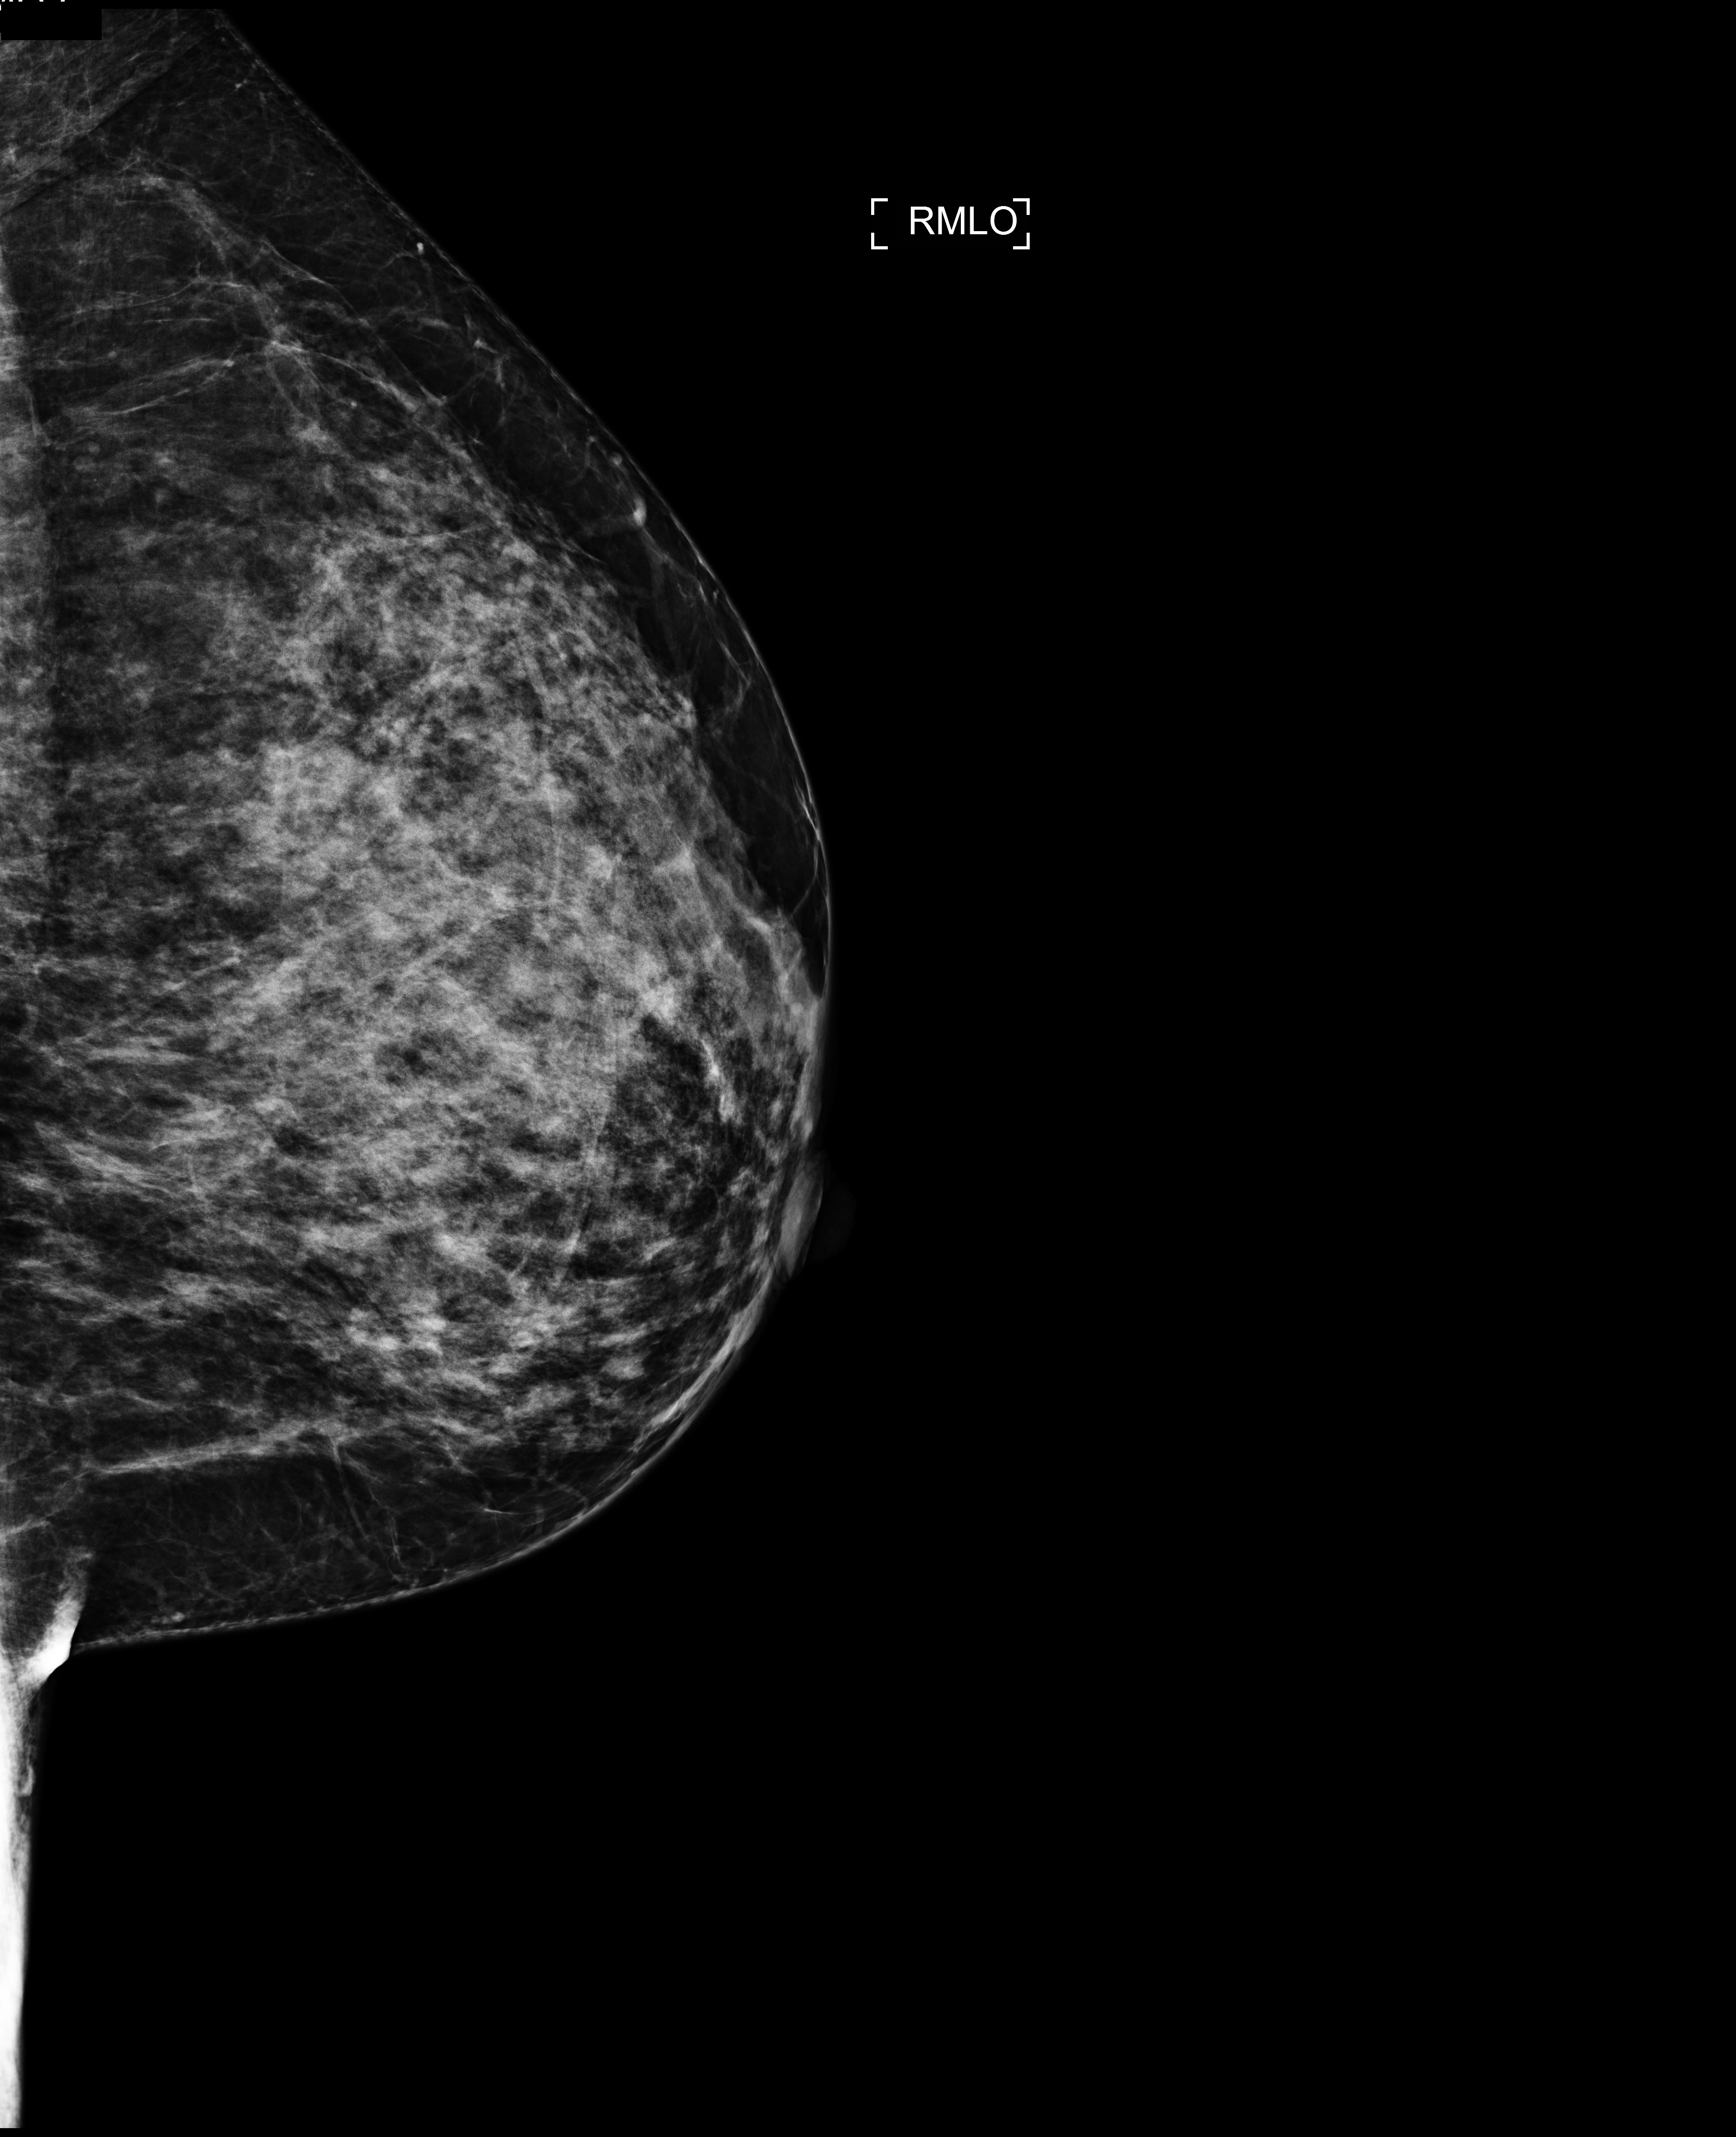
Screening examination. Patient: female, 43 years.
Image type: full-field digital mammogram. Breast: right. Projection: medio-lateral oblique projection.